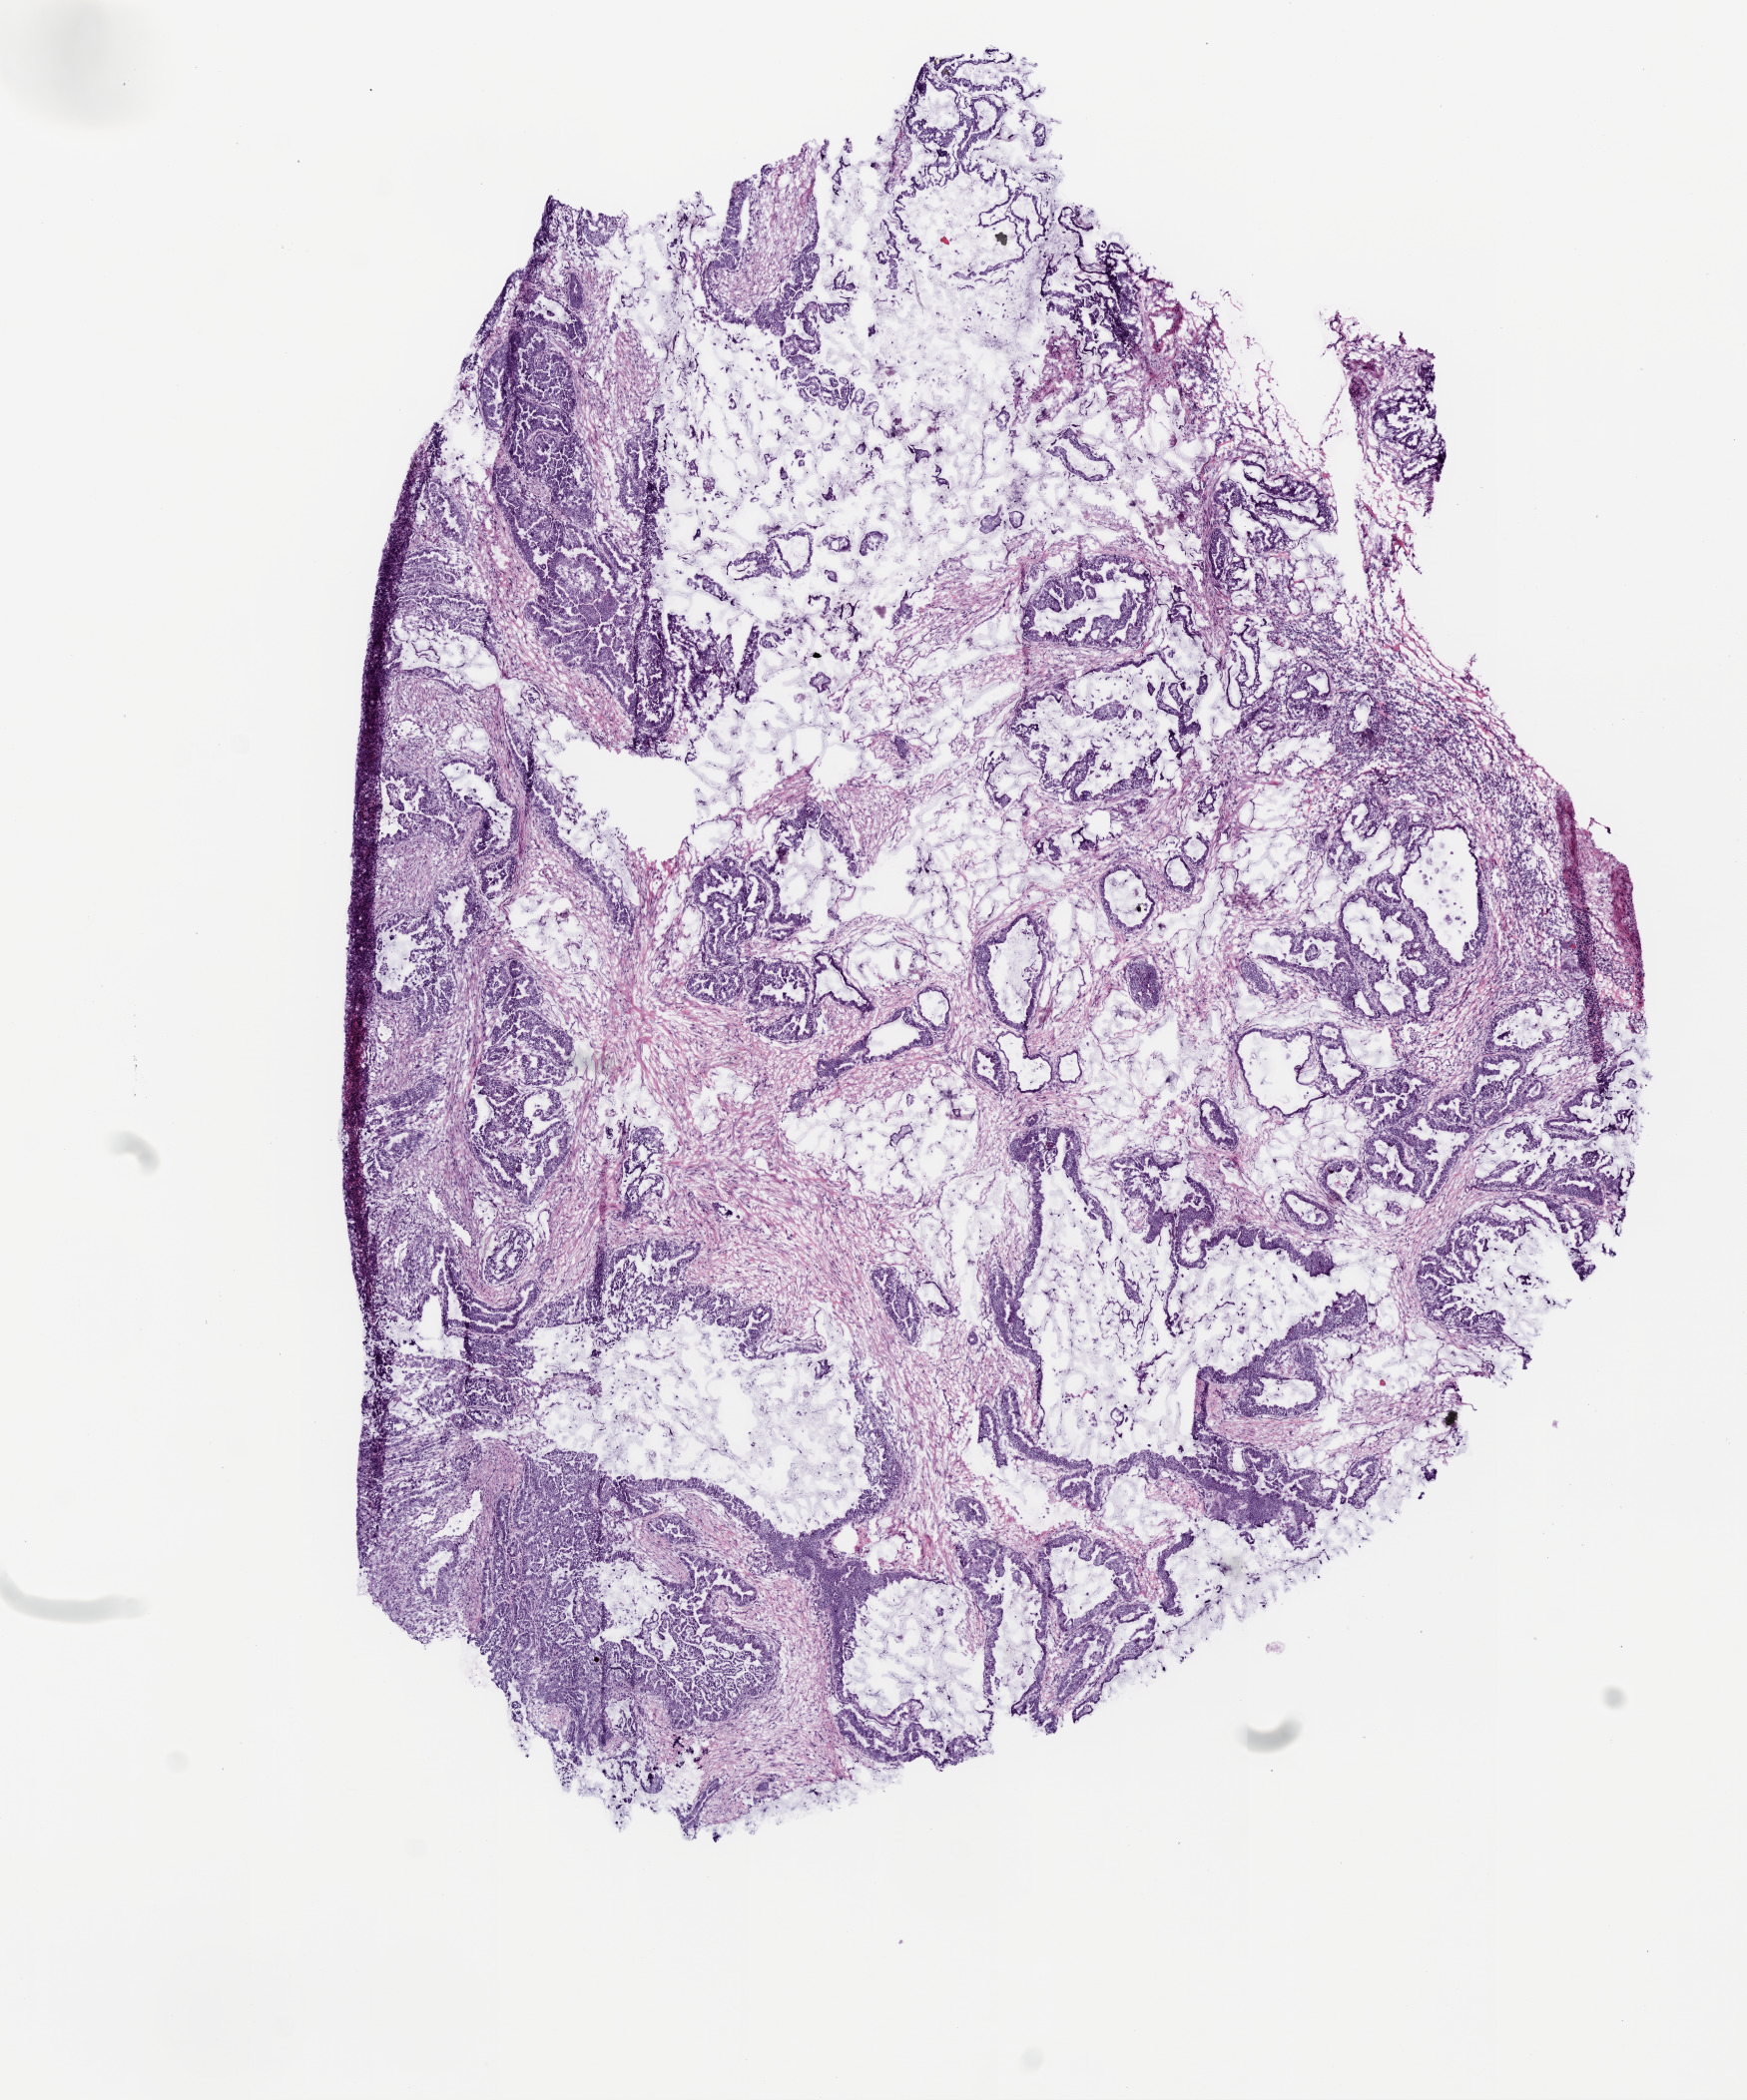
Whole-slide histology image, H&E — low-resolution overview of the scanned area, about 7.0 x 8.4 mm (acquisition: 20x scan), frozen section from the top of the tissue portion, primary tumour sample from the stomach. Patient: male, age at initial diagnosis 81 years. Histologic grade: G2 (moderately differentiated). Pathologist review of this section (percent, as recorded): tumour cells 54%, tumour nuclei 75%, normal cells 1%, stromal cells 40%, necrosis 5%.
* diagnosis: Mucinous adenocarcinoma (gastric antrum)
* TNM: T2 N1 M0
* lymph nodes positive (case pathology): 6 of 42 examined
* AJCC pathologic stage: II